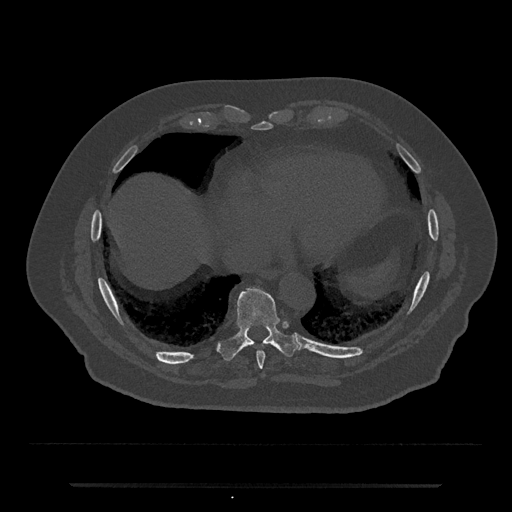
CT including the spine, one axial slice; position 770 of 797 along the scan axis; reconstruction kernel Br40s/3; bone window (W 1800 / L 400 HU); 0.5 mm slice thickness; 512 × 512 image matrix, field of view 434 × 434 mm. Male patient, age 80 years. Case-level facts recorded for this patient, not image findings: primary cancer: prostate.
Structures marked on this image (semi-automatically segmented with operator editing):
- T8 vertebra: box from (x=256, y=352) to (x=265, y=370) px
- T9 vertebra: (x=218, y=286)–(x=302, y=361)